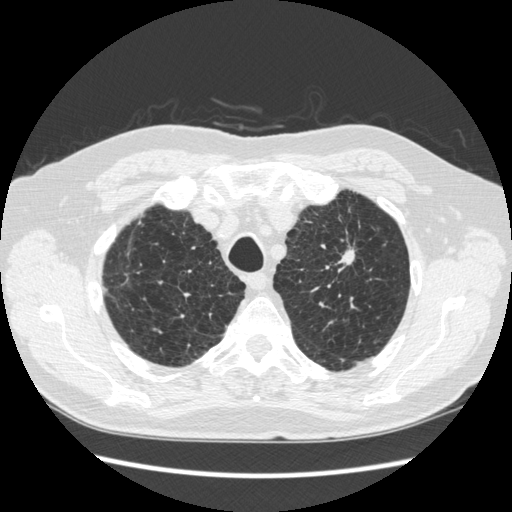
Low-dose screening chest CT, one axial slice. Slice 221 of 267 in the series (ordered by position). Reconstruction kernel STANDARD. Lung window (W 1500 / L -600 HU). 512 × 512 image matrix.
Structures marked on this image (expert manual segmentation):
- lesion 1 (tumor, upper lobe of left lung): box from (x=340, y=240) to (x=355, y=265) px